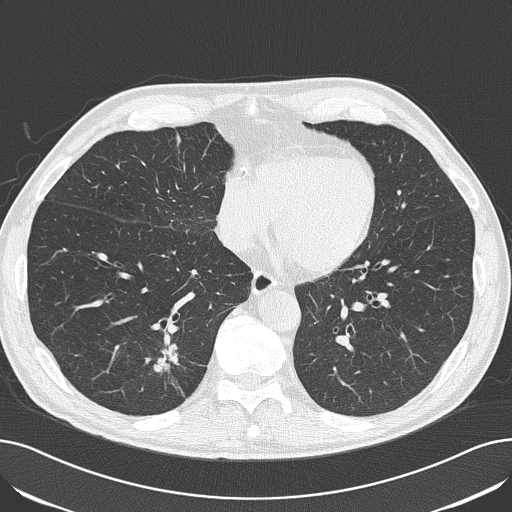
Low-dose screening chest CT, one axial slice; position 62 of 182 along the scan axis; lung window (W 1500 / L -600 HU); 512 × 512 image matrix, field of view 368 × 368 mm.
Outlined on this slice (manually delineated by an expert):
- lesion 1 (tumor, lower lobe of right lung): bounding box <154,345,178,372> (left, top, right, bottom; pixels)